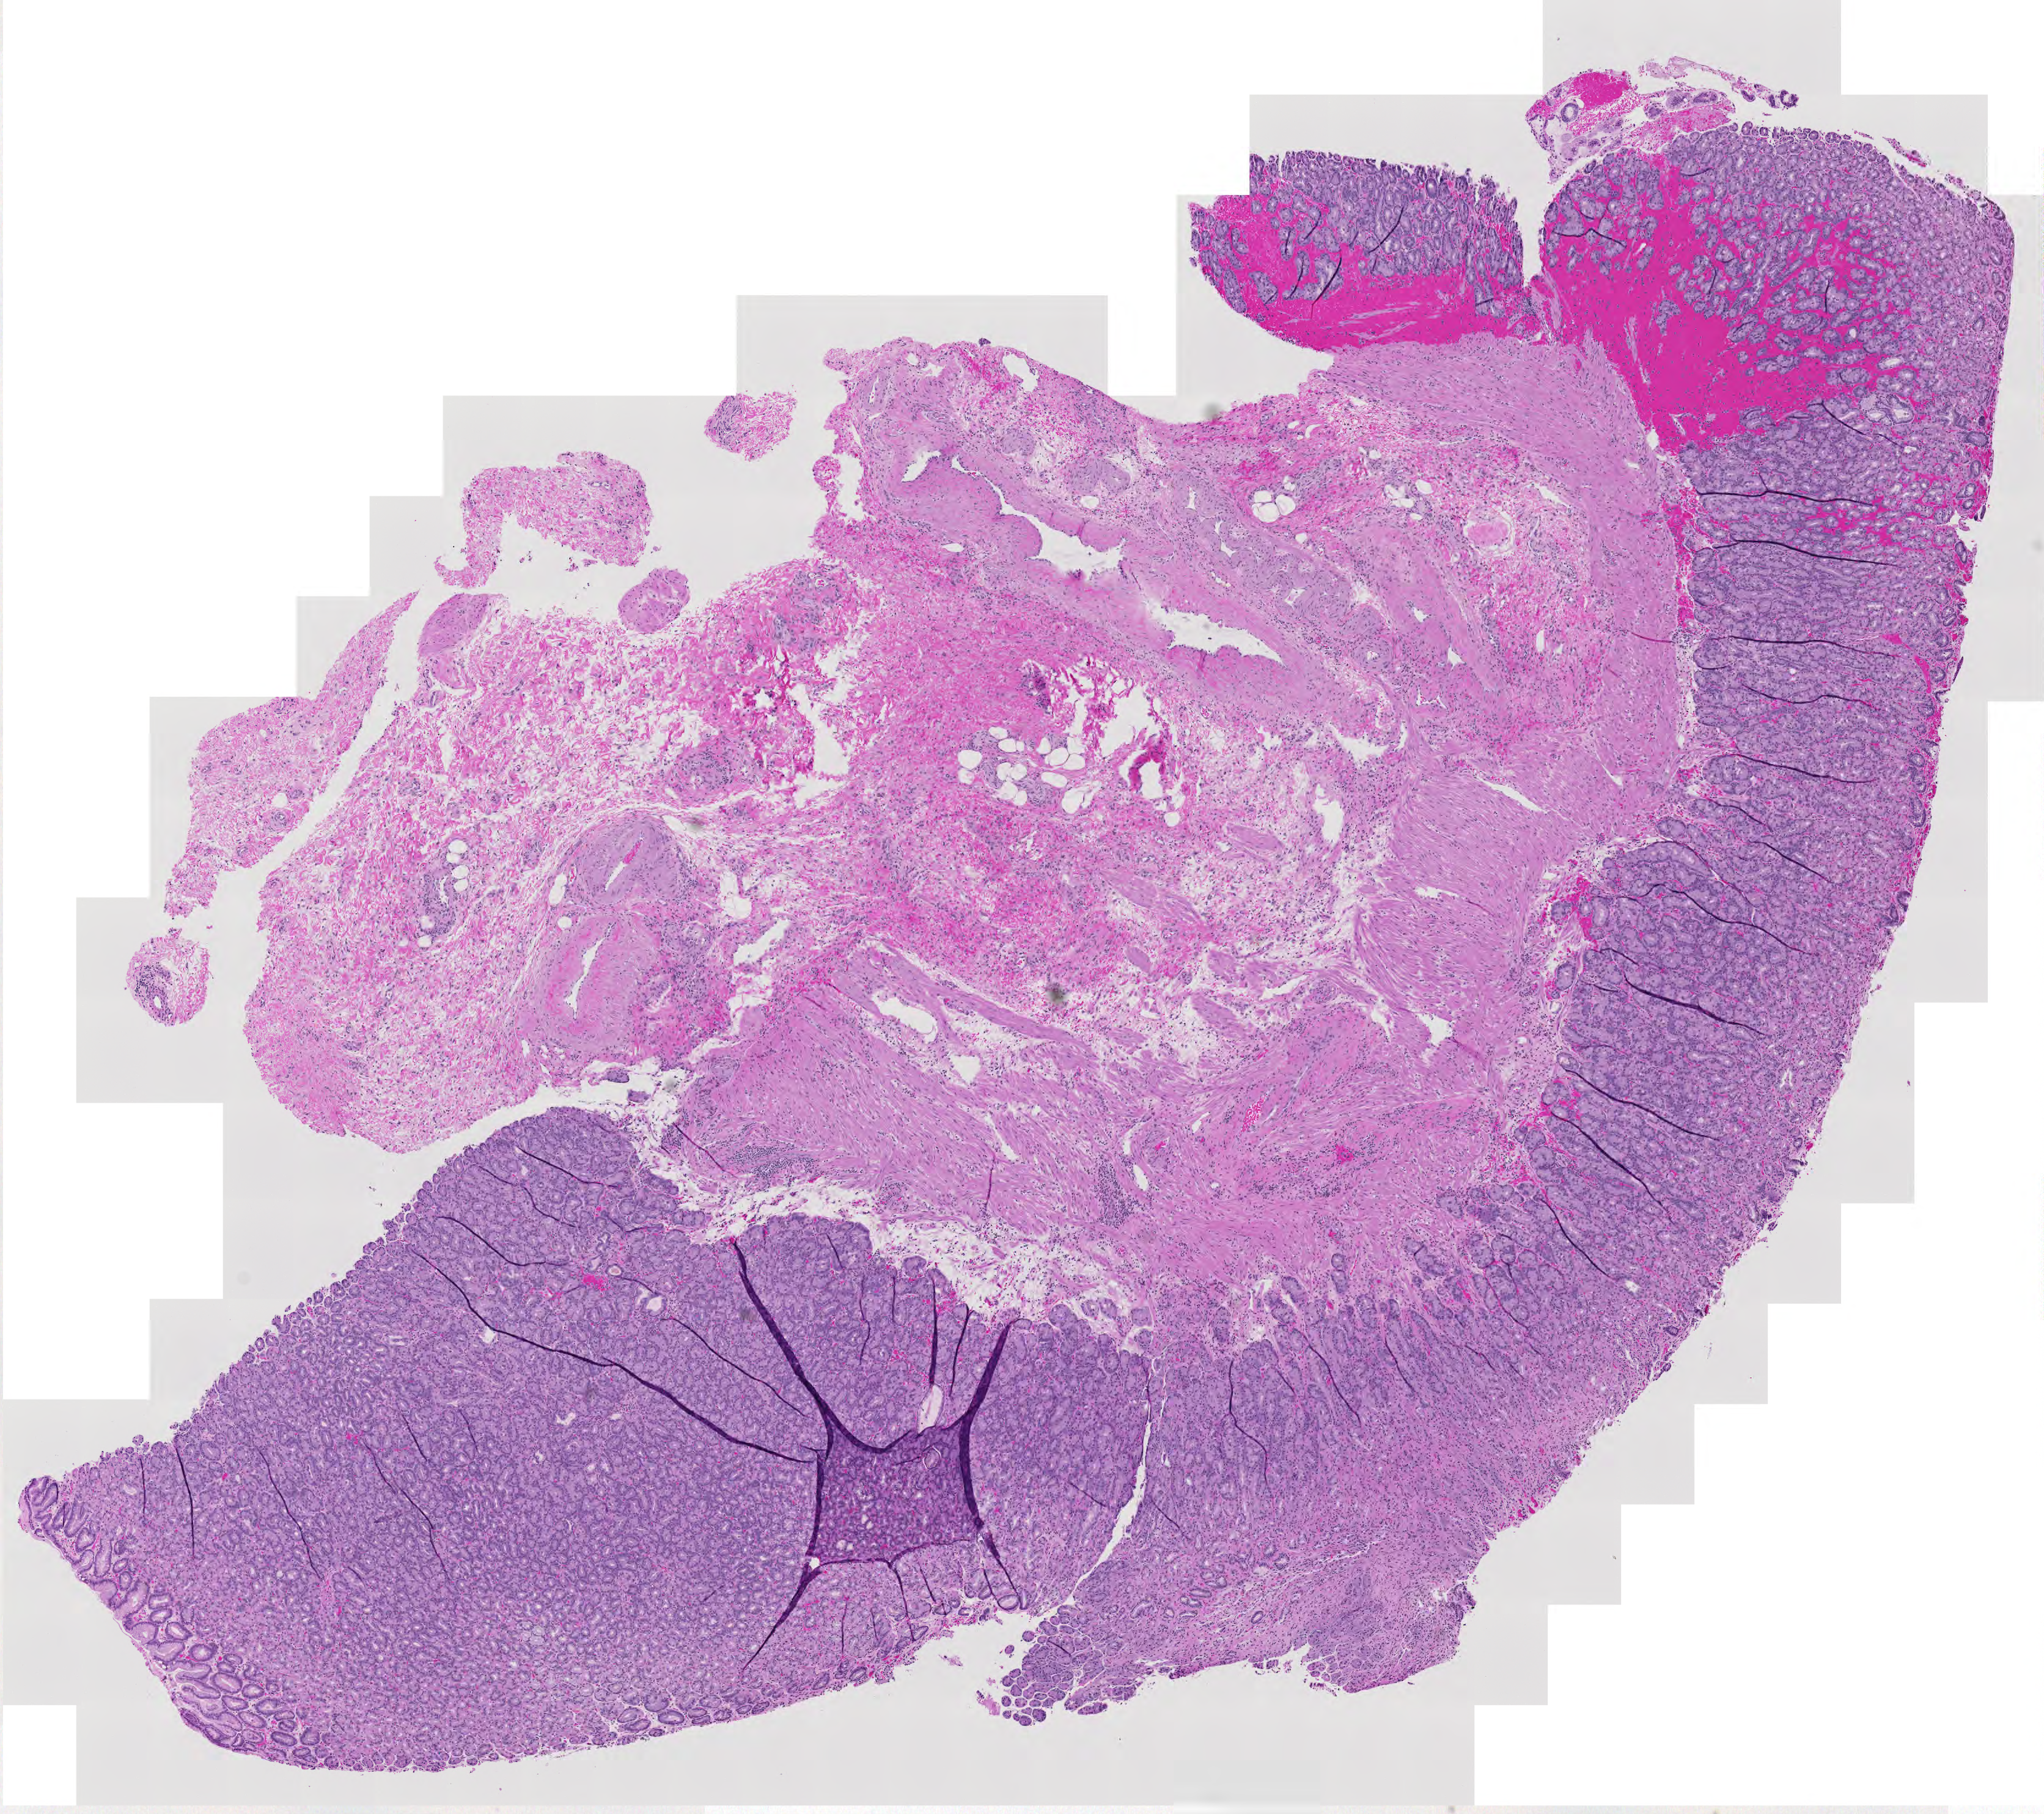
Digitized Hematoxylin and eosin (H&E) stained tissue section (whole slide) — a low-resolution overview of the entire scanned area, about 8.6 x 7.7 mm (acquisition: 20x scan). Patient: male, age 87 years.
* patient diagnosis (cohort enrolment): sarcoma (site not recorded at cohort level)